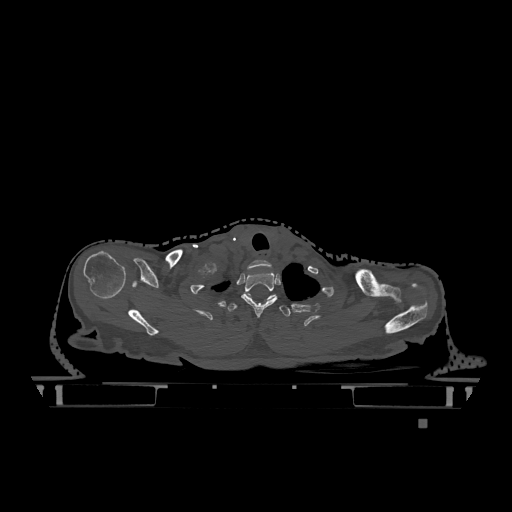
CT including the spine, one axial slice; slice 991 of 1317 in the series (ordered by position); bone window (W 1800 / L 400 HU); 0.5 mm slice thickness; 512 × 512 image matrix. Patient: female, 74 years. From the clinical record (not read from this slice): primary cancer: lung; vertebrae with lytic lesions (as recorded): T1, T4, T5, T6, L4, L5.
Structures marked on this image (semi-automatic segmentation, software-assisted and operator-edited):
- T1 vertebra: bounding box <241,271,278,317> (left, top, right, bottom; pixels)
- T2 vertebra: <228,295,291,317>